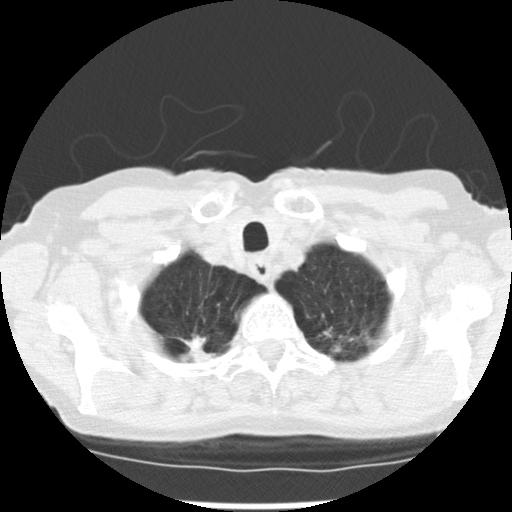
Chest CT (low-dose screening protocol), one axial image; first (baseline) screen; lung window (W 1500 / L -600 HU); slice 21 of 265 in the series; 512 × 512 image matrix. Female participant, aged 72 years at enrolment.
Expert reader's lesion annotation, bounding box (x1, y1, x2, y2) in pixels: (166, 317, 231, 364). The screening reader recorded 3 non-calcified nodules or masses ≥4 mm on this exam (right upper lobe, left upper lobe, left lower lobe); which of them this box marks is not recorded. Official screen result: positive, change unspecified: nodule(s) >= 4 mm or enlarging nodule(s), mass(es), or other non-specific abnormalities suspicious for lung cancer. Lung cancer was diagnosed 50 days after this screen: adenocarcinoma, NOS, right upper lobe, moderately differentiated (G2), stage IB (AJCC 6th edition), 22 mm at pathology.